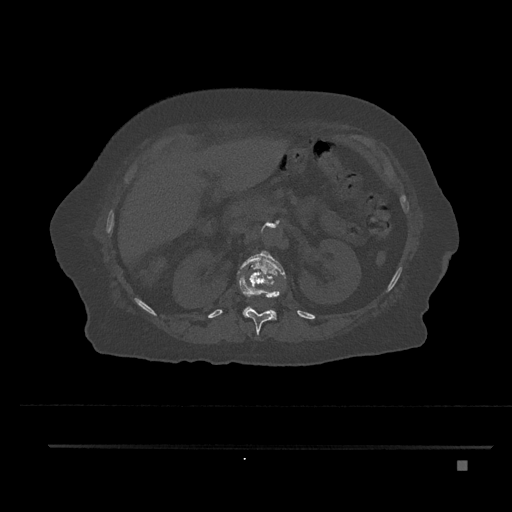
CT including the spine, one axial slice. Position 246 of 797 along the scan axis. Reconstruction kernel Br40s/3. 120 kVp. Bone window (W 1800 / L 400 HU). 512 × 512 image matrix, field of view 437 × 437 mm. Female patient, age 76 years. From the clinical record (not read from this slice): primary cancer: lung.
Annotated regions visible in this slice (semi-automatically segmented with operator editing):
- L1 vertebra: bounding box [x1, y1, x2, y2] px = [238, 252, 286, 319]
- T12 vertebra: [239, 273, 281, 335]